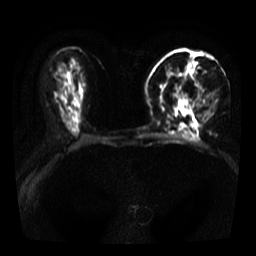
Breast MRI, one axial slice; diffusion-weighted series; image 2 of 4 stored at this slice position (different b-values; order by instance number); 3 T; 5 mm slice thickness; 256 × 256 image matrix, field of view 320 × 320 mm. Female patient.
Outlined on this slice (manually delineated by an expert):
- tumour on diffusion-weighted imaging: box from (x=161, y=86) to (x=187, y=100) px